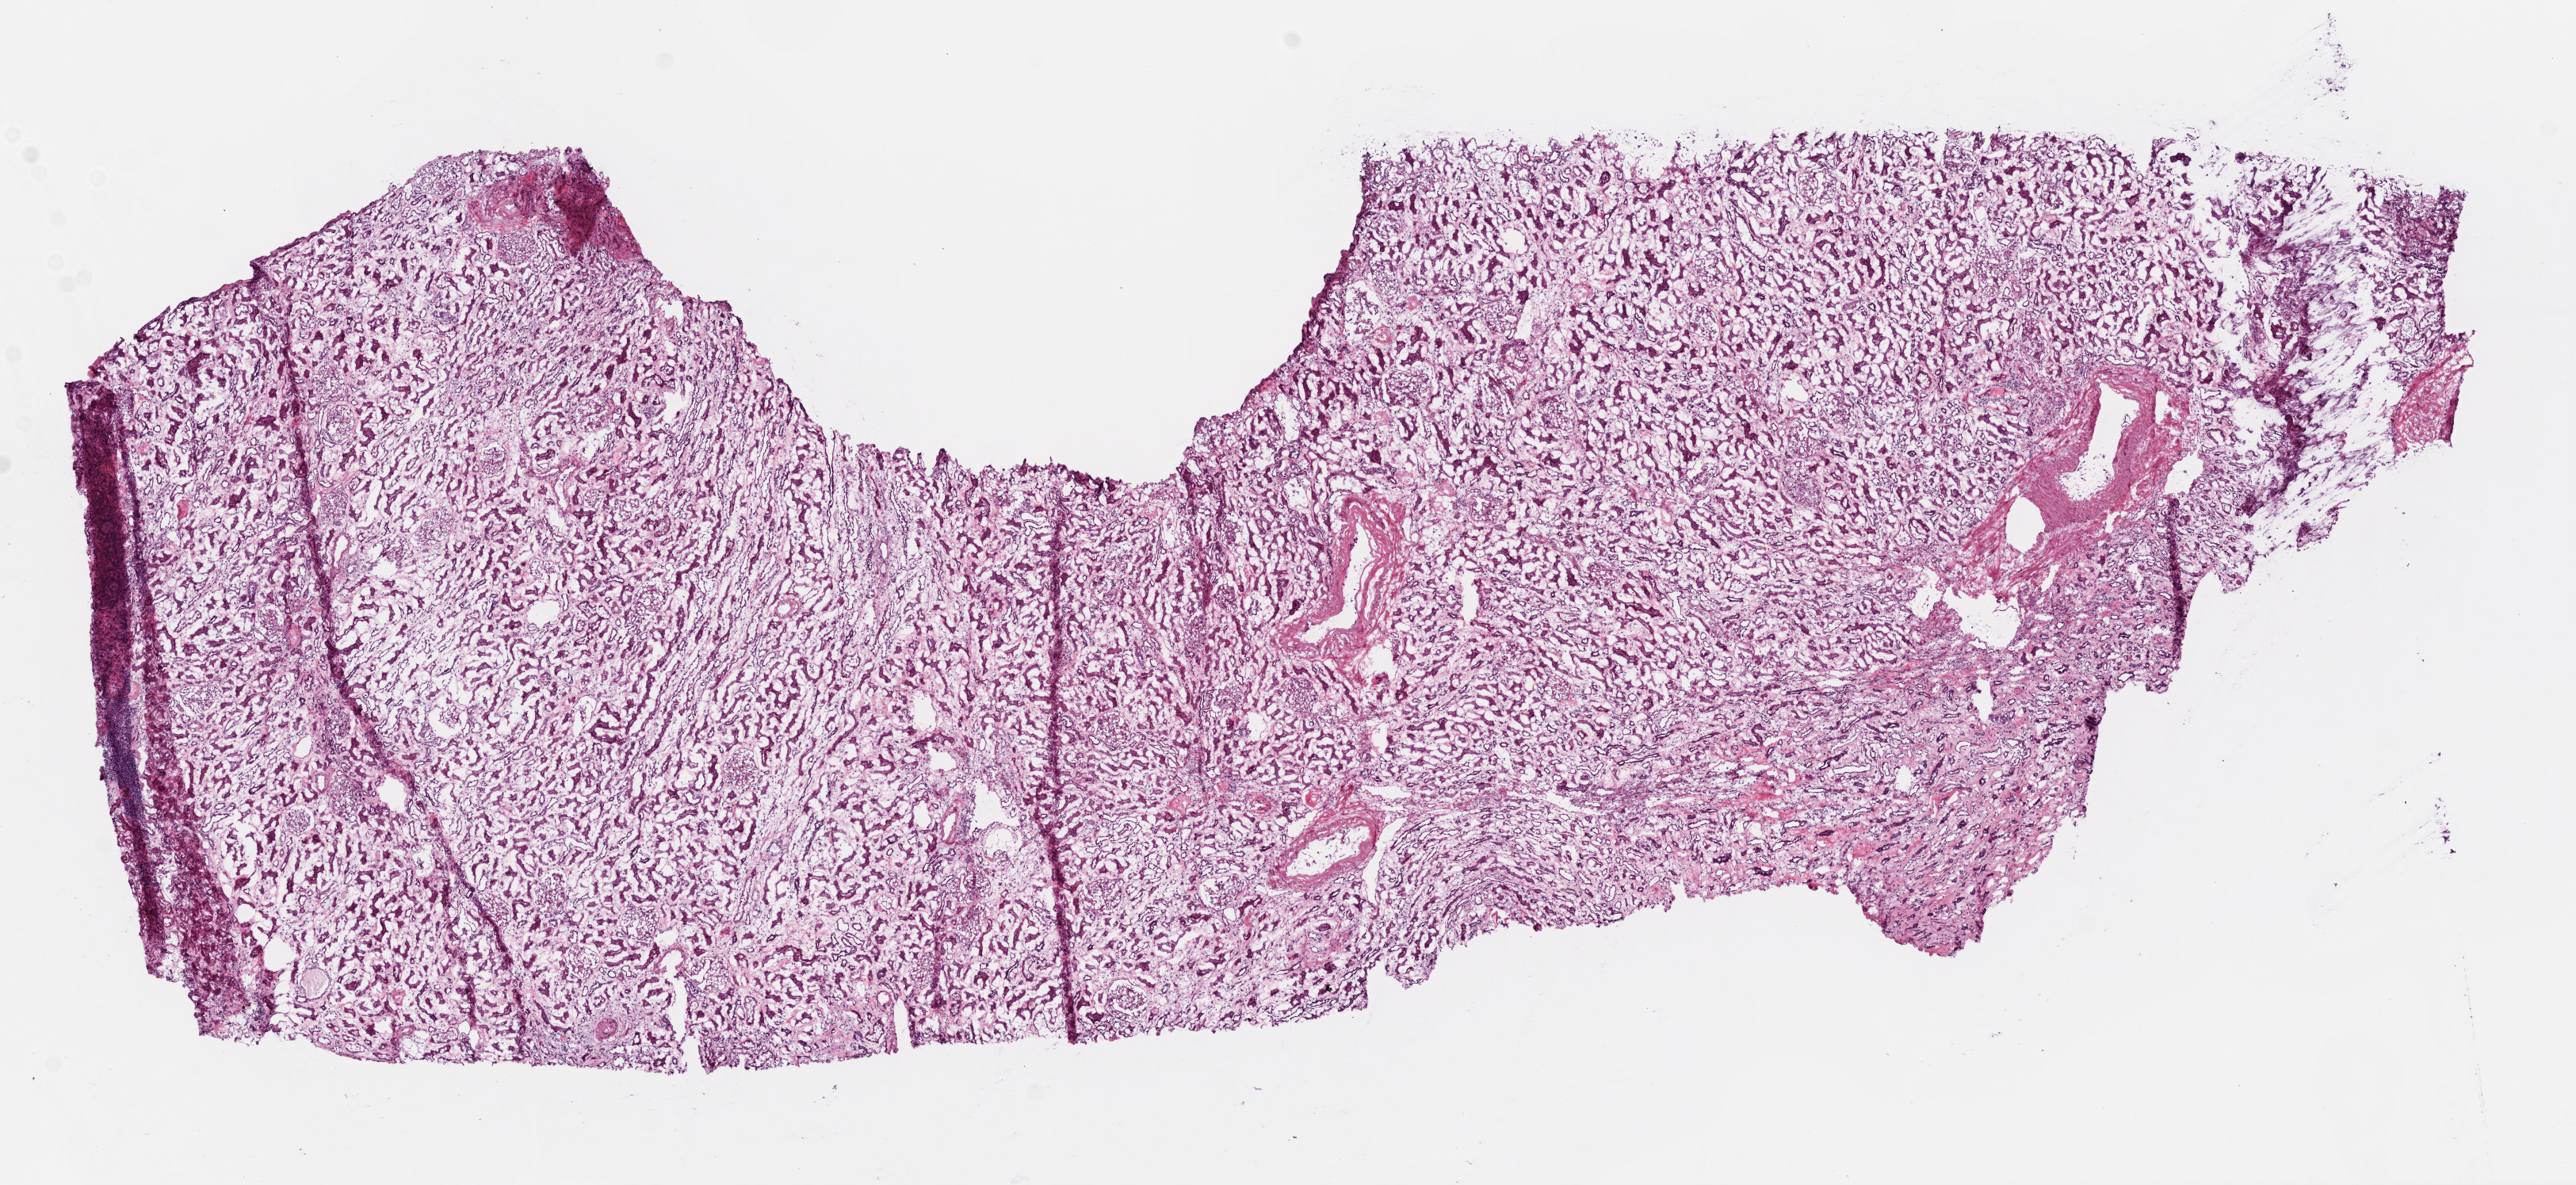
Hematoxylin and eosin (H&E) stained whole-slide image, a low-resolution overview of the entire scanned area, about 13.0 x 6.0 mm (from a 20x scan), frozen section from the top of the tissue portion, solid tissue normal (non-tumour tissue) sample from the kidney. Patient: male, age at initial diagnosis 79 years.
This section: solid tissue normal sample (biorepository sample class). Patient diagnosis: Clear cell adenocarcinoma, NOS.